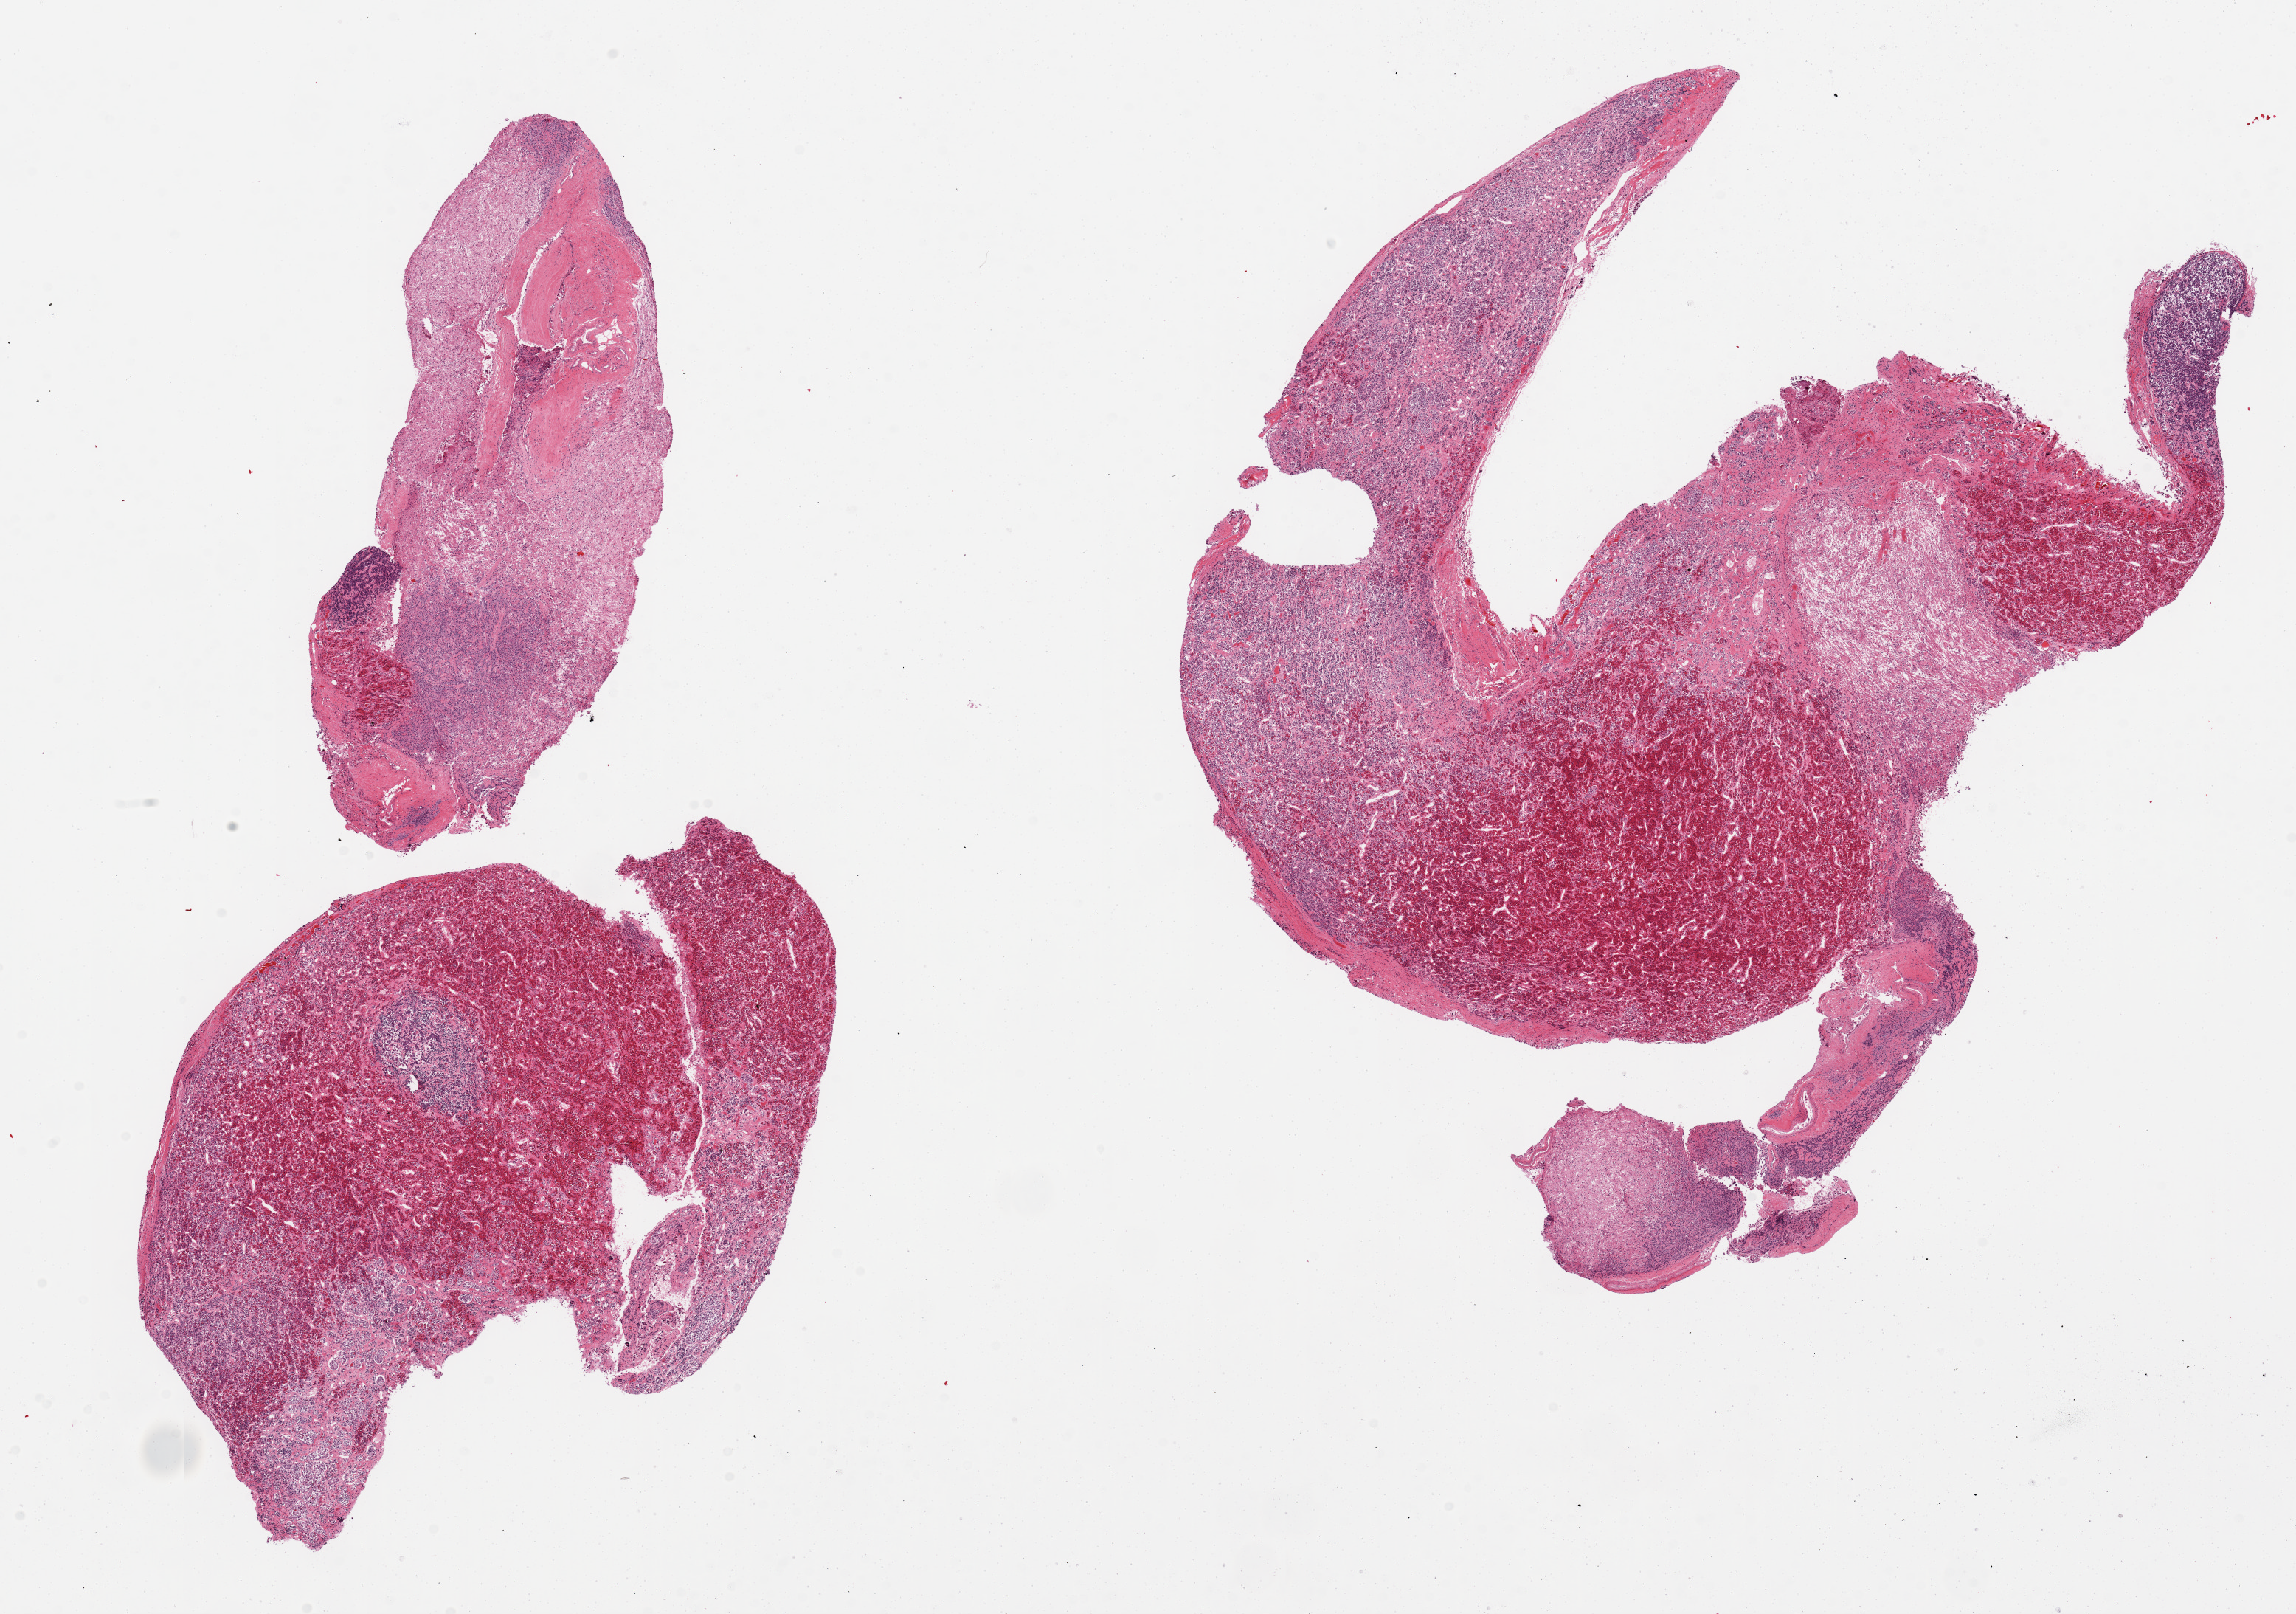
Digitized haematoxylin and eosin-stained section, brightfield, whole scanned area (about 24.6 x 17.3 mm, slide scanned at 20x) shown as a low-resolution overview, PAXgene-fixed, paraffin-embedded tissue, section of pituitary (target tissue), tissue donor sample. Male donor.
Review note (as recorded): 3 pieces; anterior and posterior.